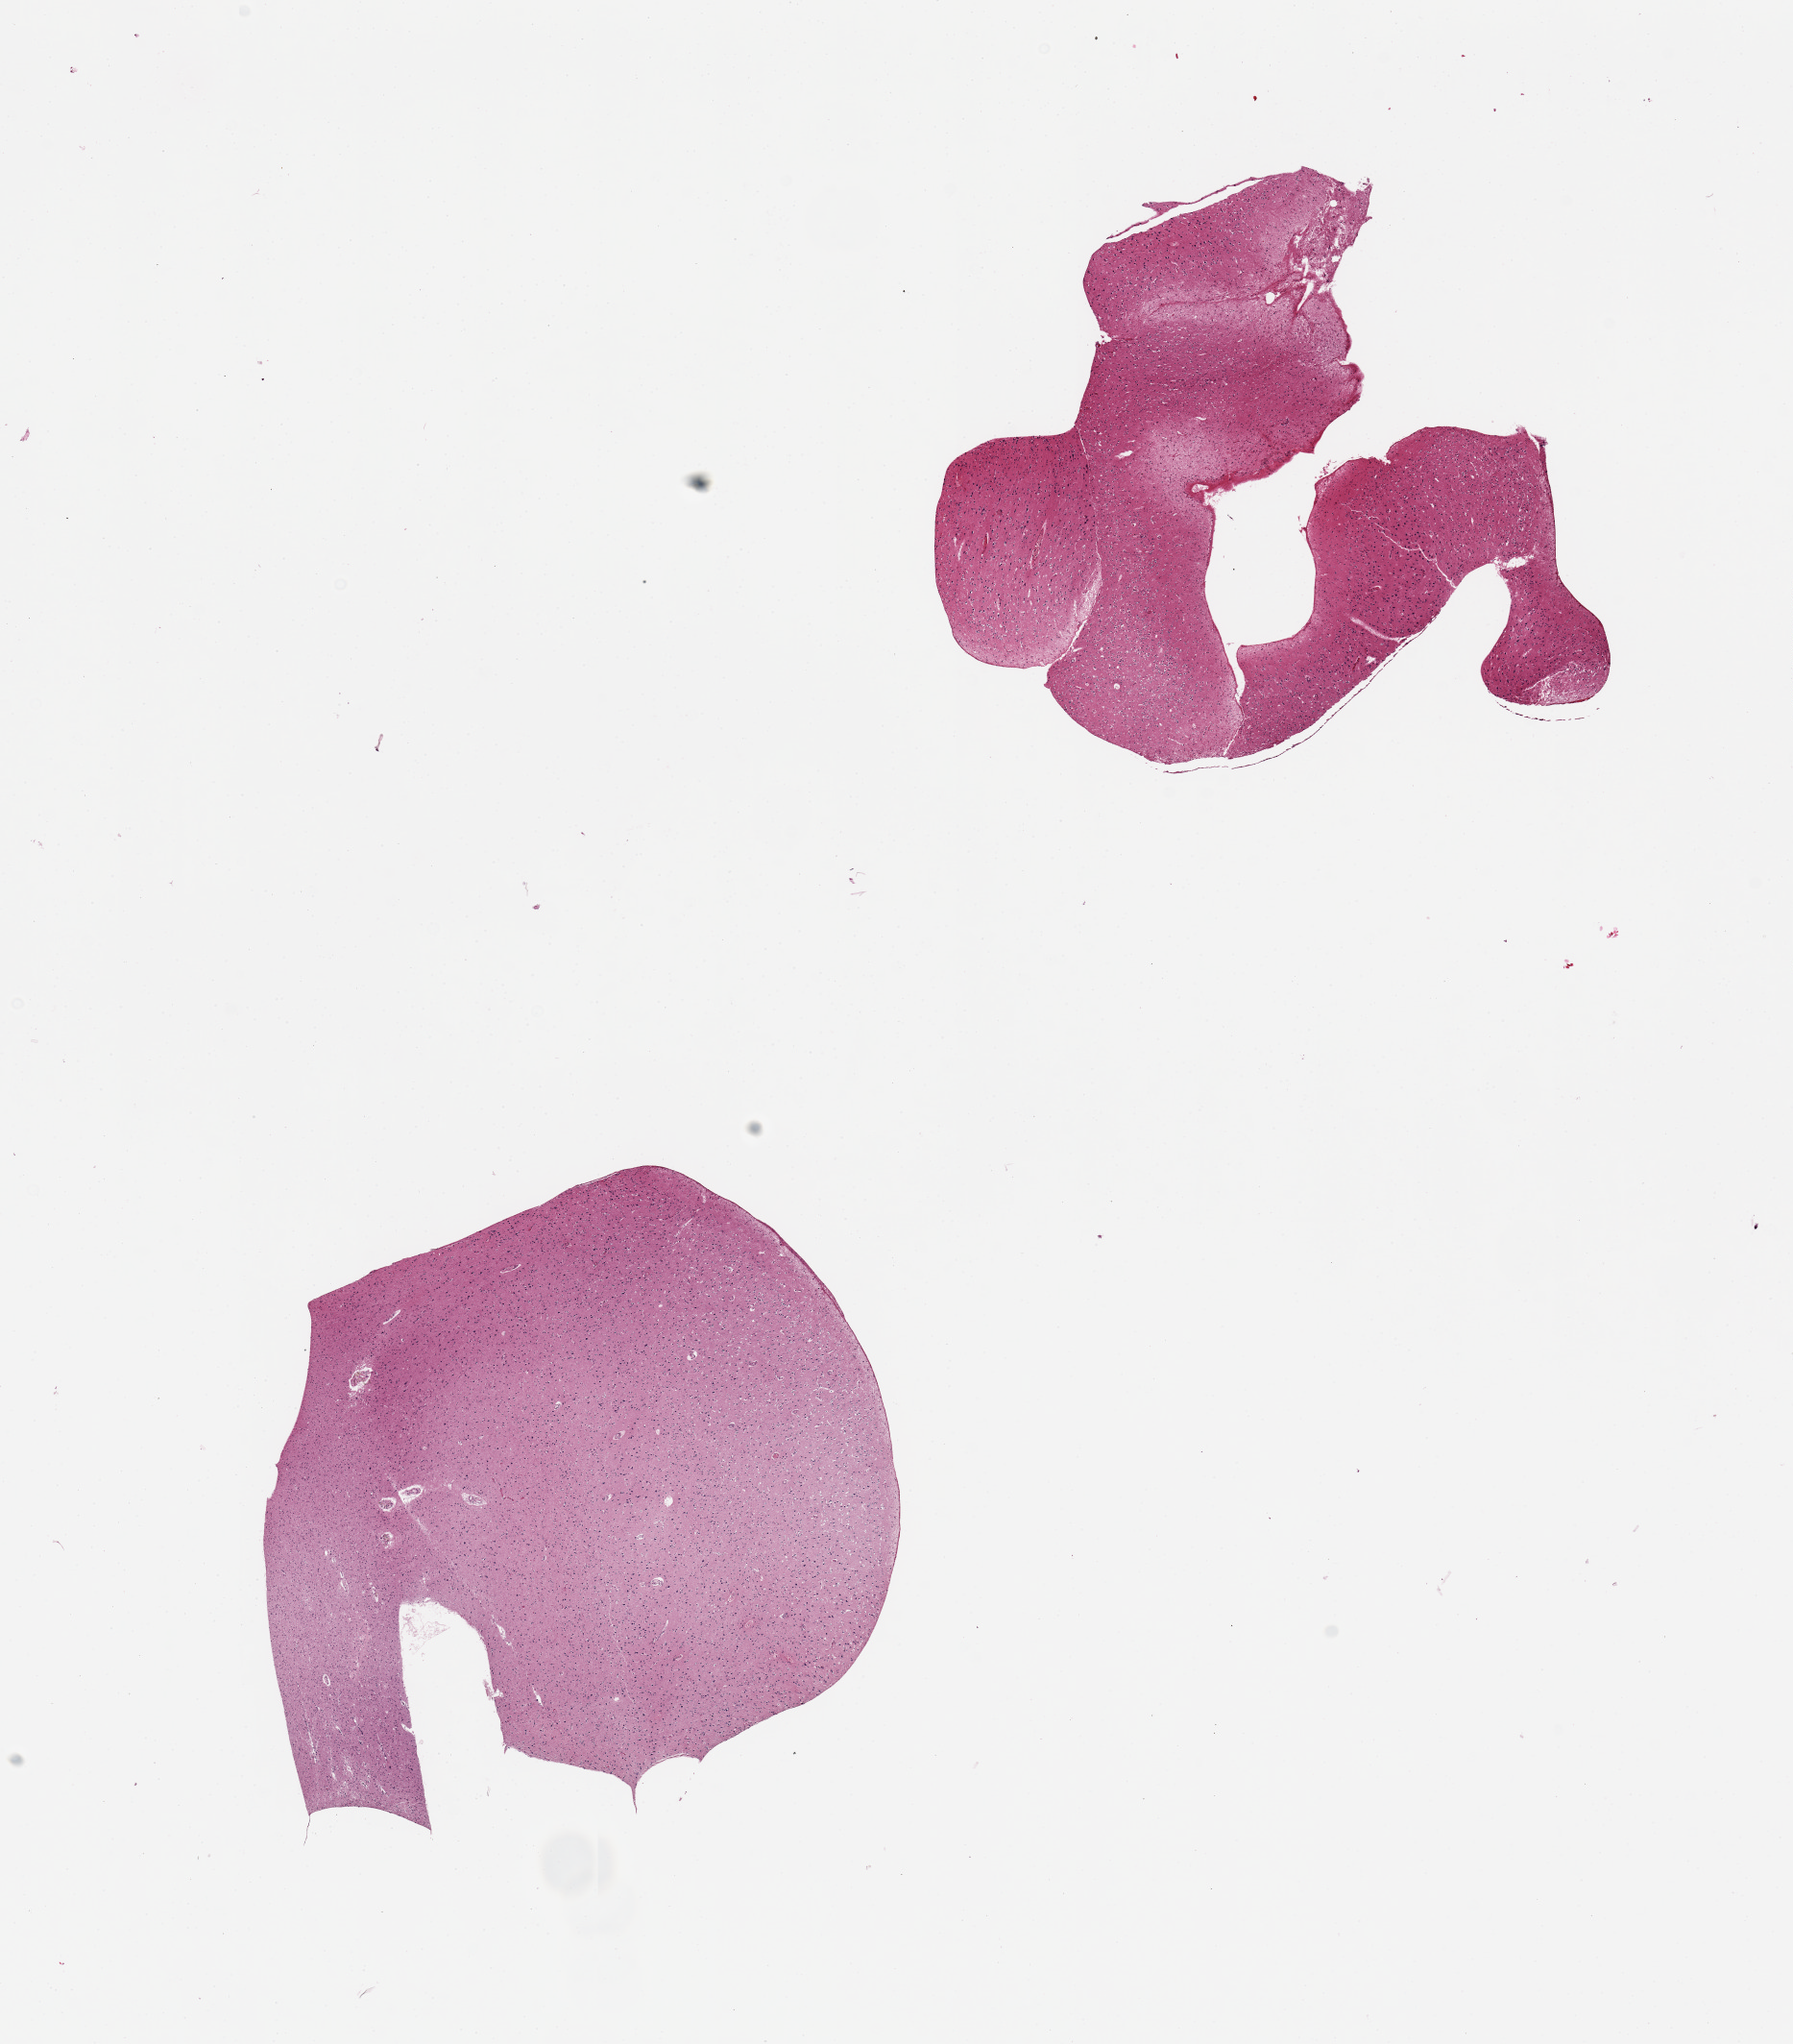
Whole-slide image, haematoxylin and eosin stain, shown as a low-resolution overview of the whole scanned area (about 14.8 x 16.8 mm); PAXgene-fixed paraffin-embedded (PFPE) section; target tissue: cerebral cortex; donor tissue sample.
• review note (as recorded): 2 pieces; CEREBRUM NOT CEREBELLUM (as originally labeled)